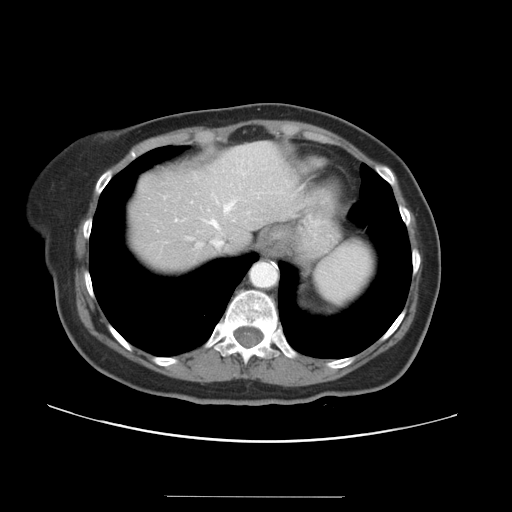
Contrast-enhanced abdominal CT, one axial slice; slice 29 of 34 in the series (ordered by position); reconstruction kernel STANDARD; 120 kVp; intravenous contrast given; soft-tissue window (W 400 / L 40 HU); 5 mm slice thickness; 512 × 512 image matrix, field of view 382 × 382 mm. Female patient, age 69 years. From the clinical record (not read from this slice): diagnosis: colorectal cancer liver metastases, imaged before liver resection.
Annotated regions visible in this slice (outlined manually by an expert reader):
- hepatic veins: box from (x=187, y=201) to (x=234, y=247) px
- liver: (x=130, y=143)–(x=303, y=272)
- planned liver remnant (the part of the liver to remain after resection): (x=130, y=143)–(x=303, y=272)